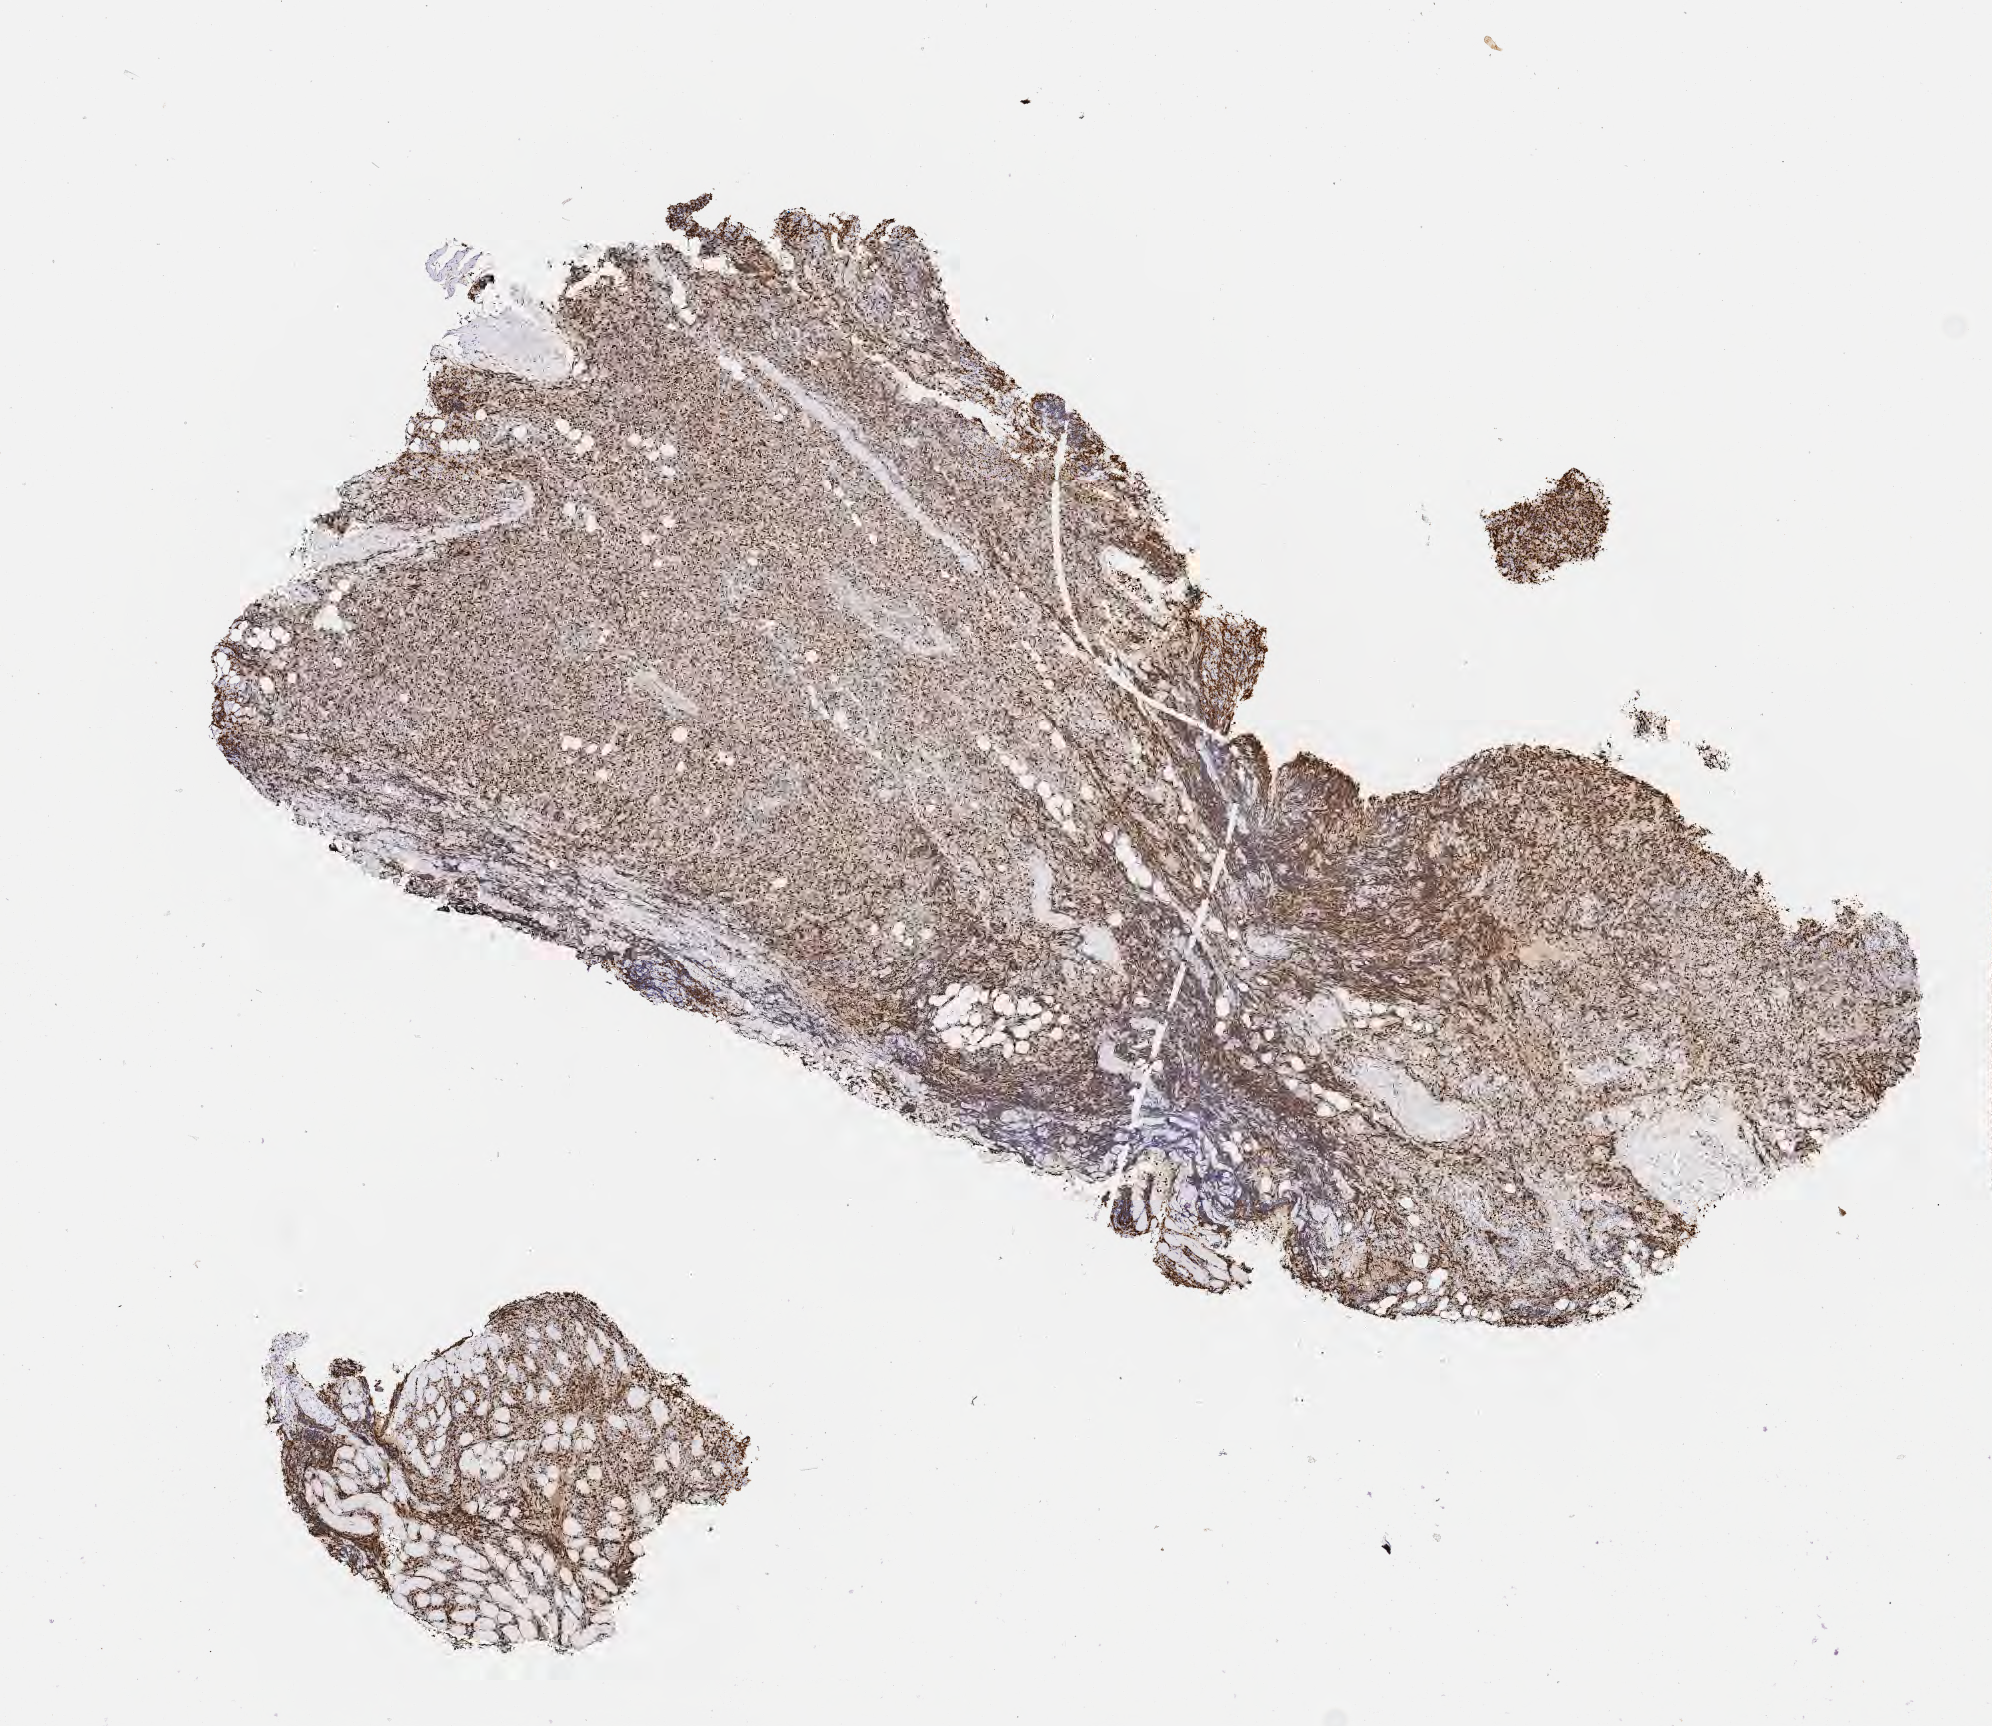
Whole-slide image, immunohistochemical stain for Ki-67, whole scanned area (about 8.0 x 7.0 mm) shown as a low-resolution overview, tumor tissue. Patient male; aged 67.
Diagnosis: Diffuse large B-cell lymphoma, NOS.